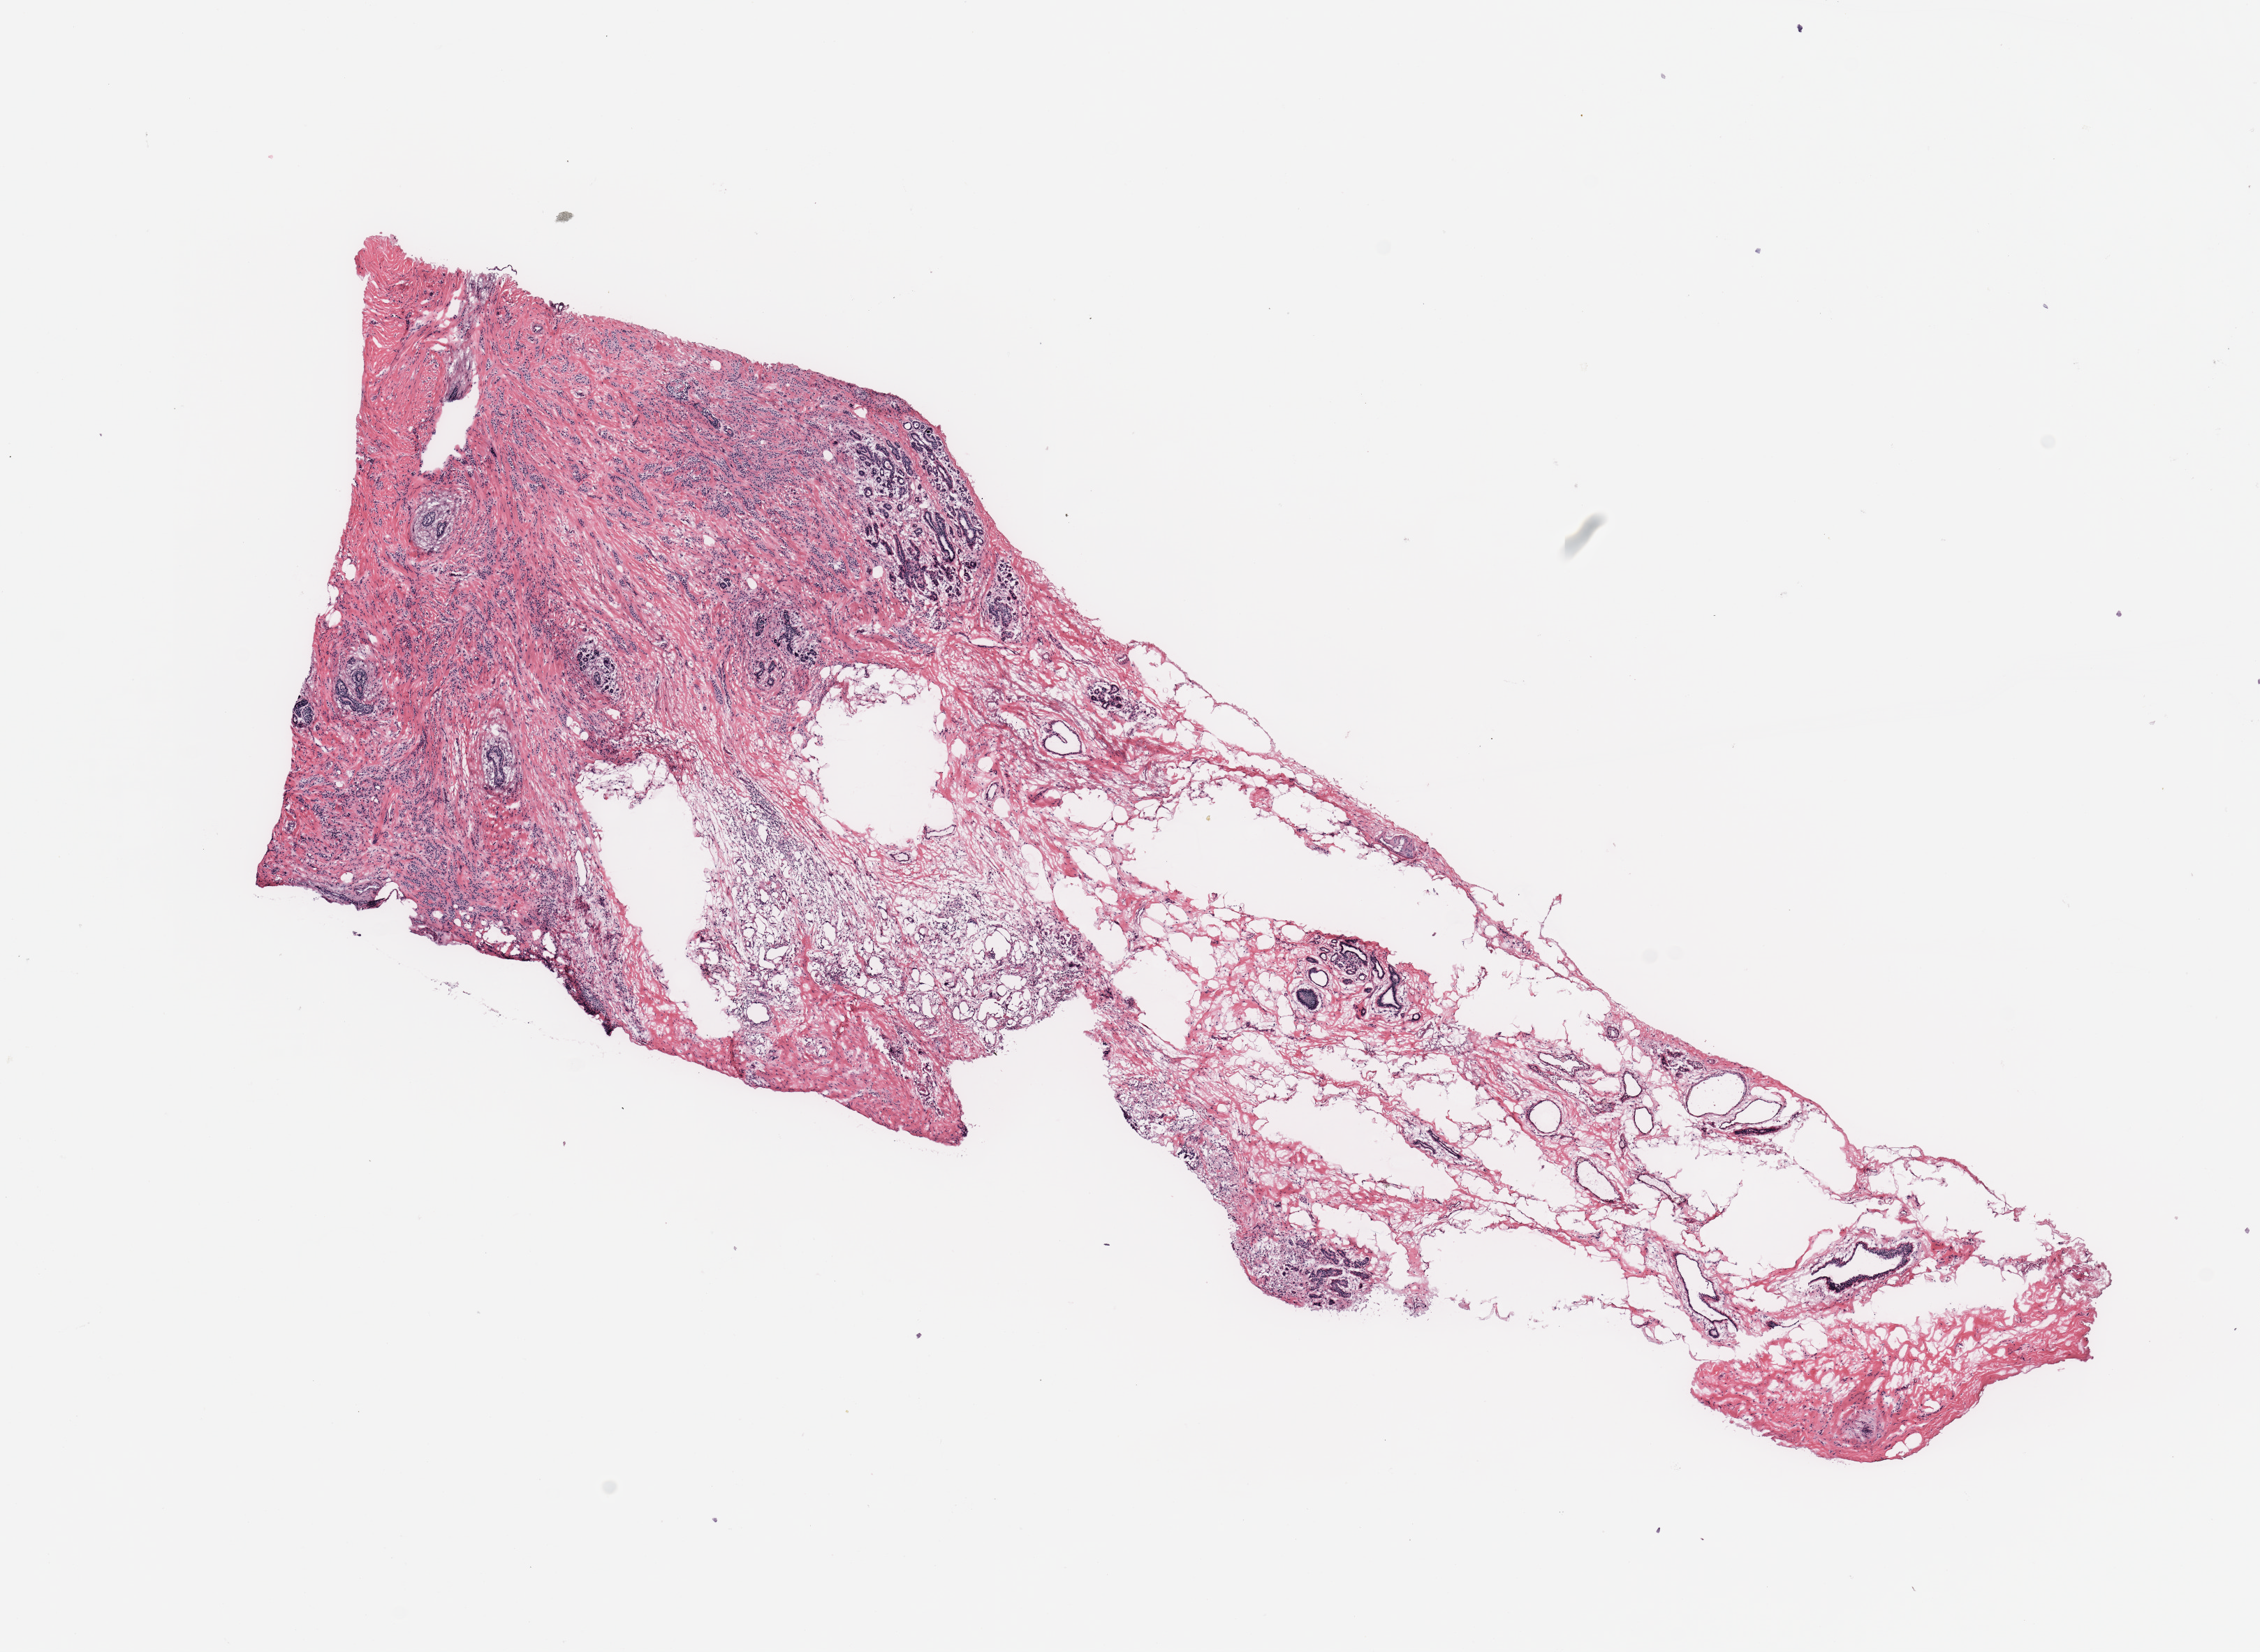
Whole-slide histology image, H&E, a low-resolution overview of the entire scanned area, about 12.8 x 9.4 mm (from a 20x scan); breast, tissue type not recorded.
Patient diagnosis (cohort enrolment): breast cancer (breast).